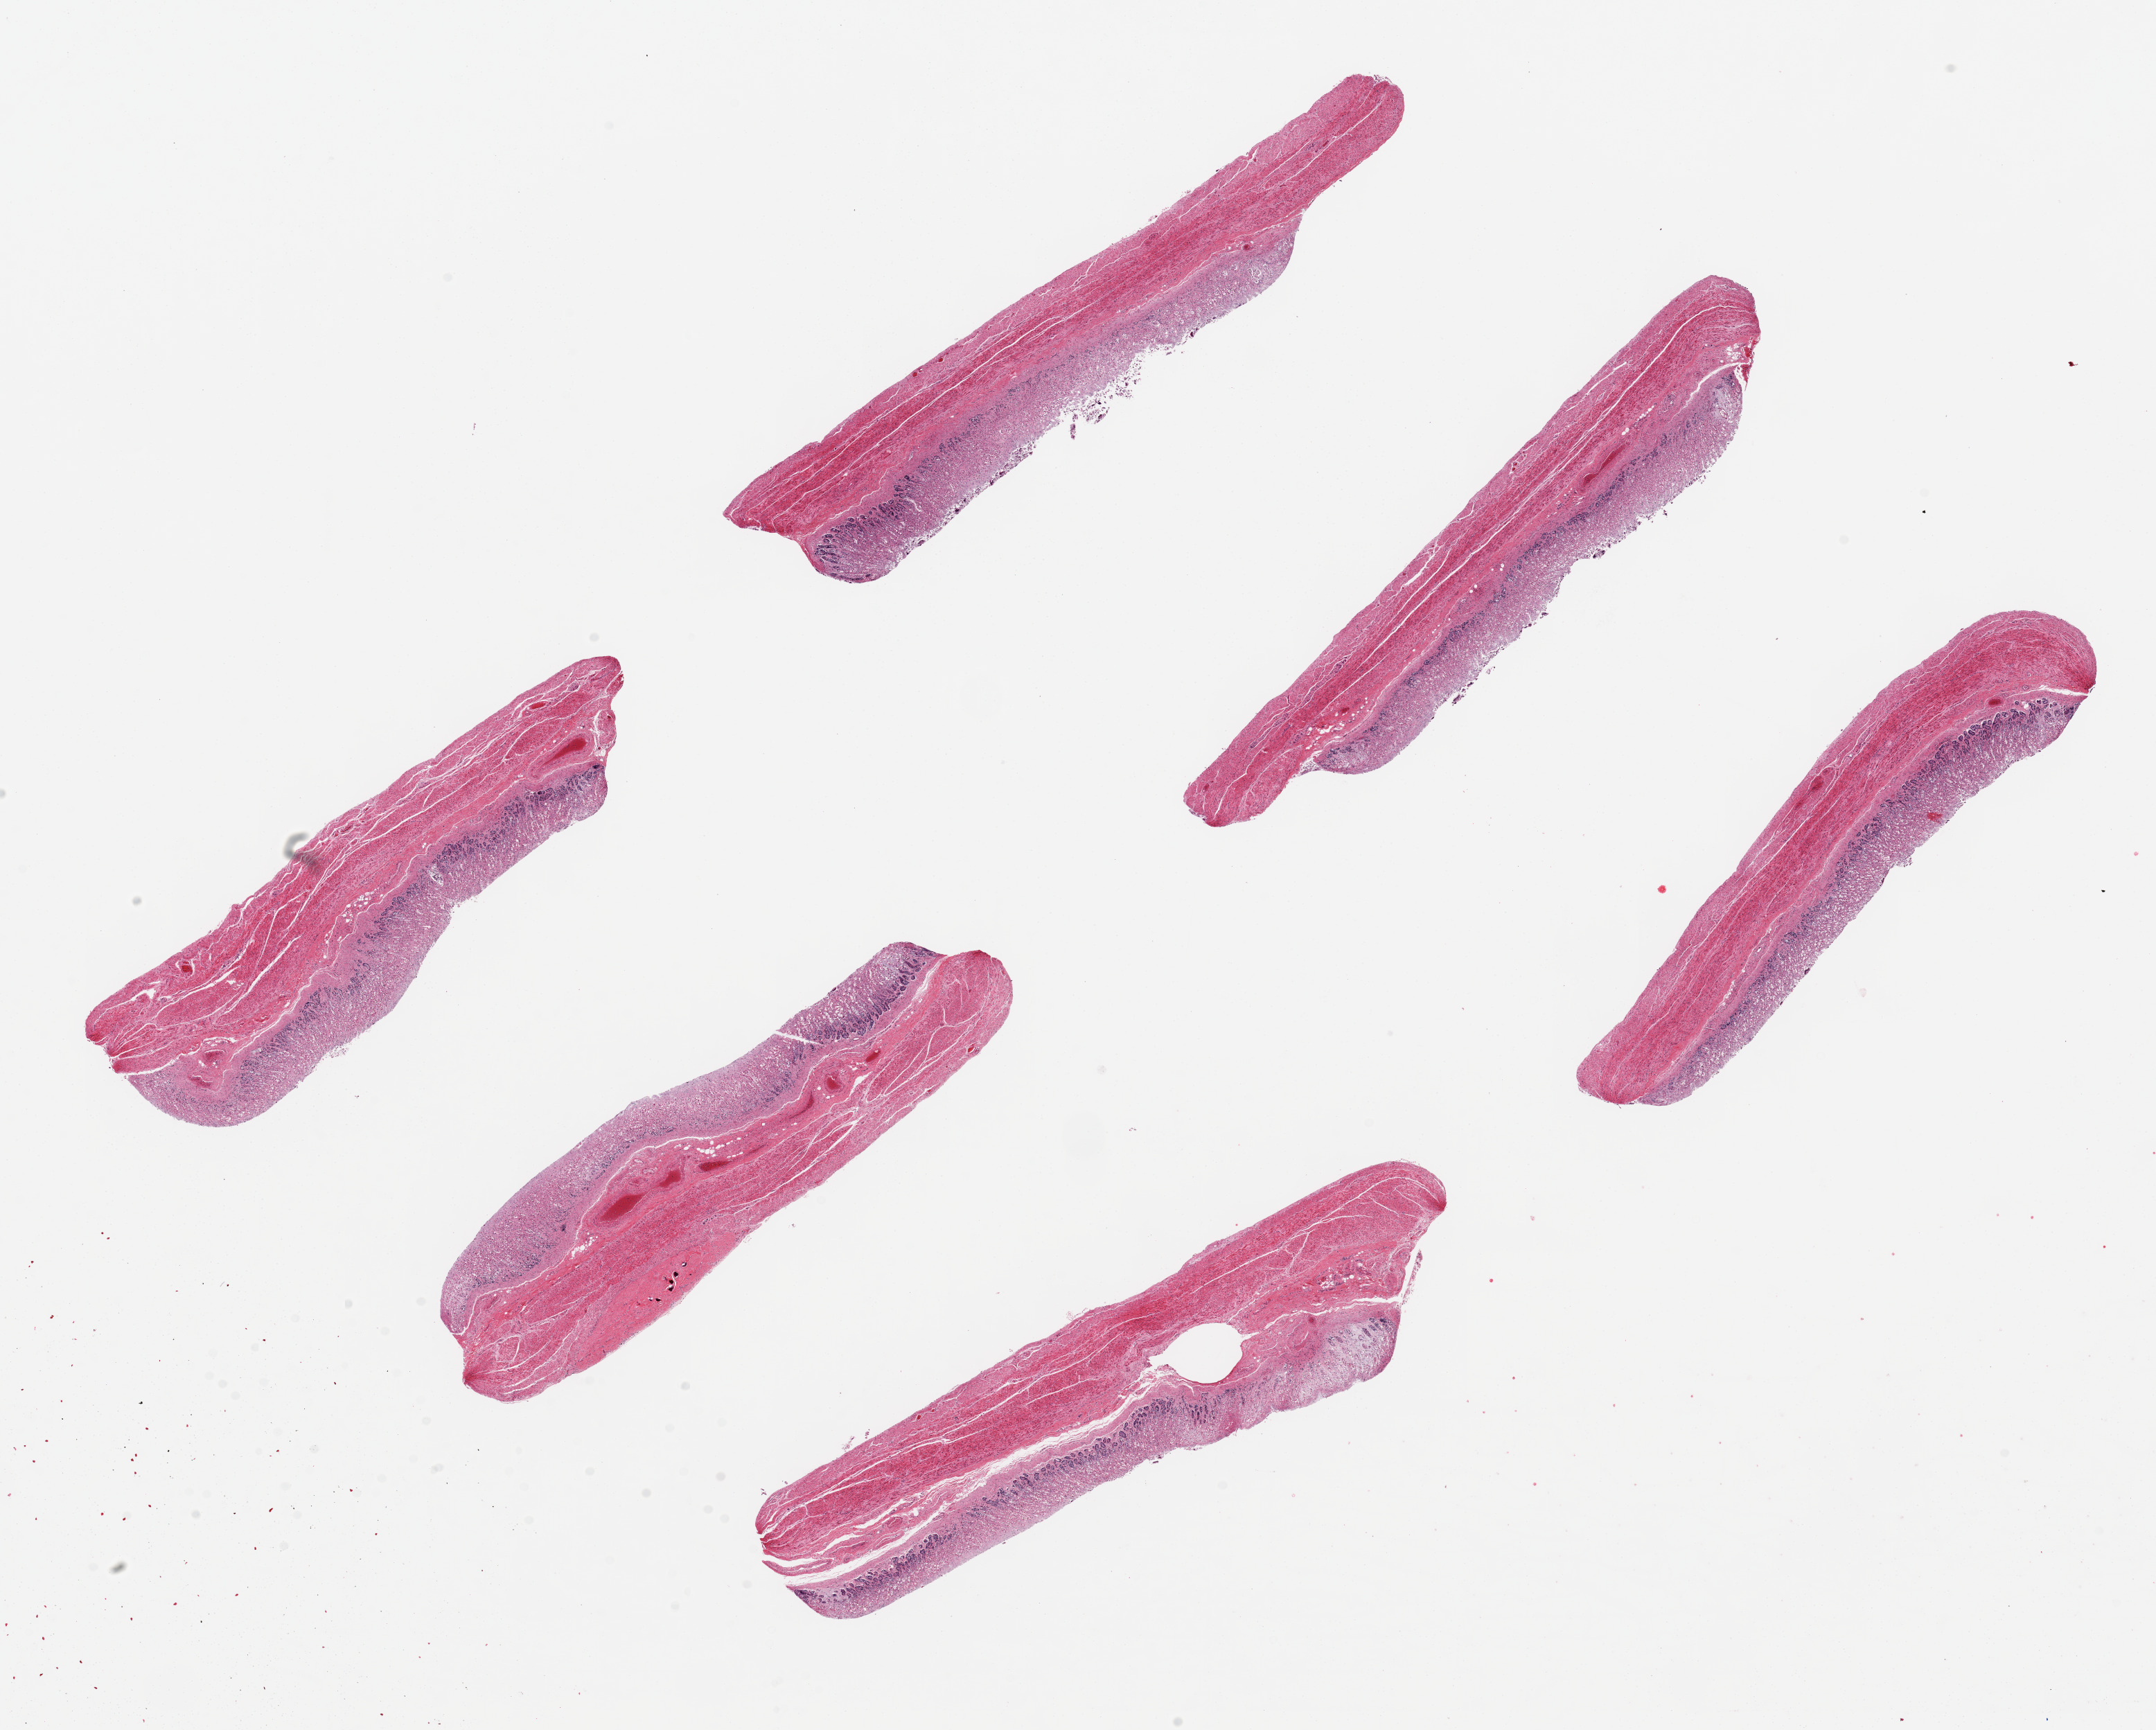
Haematoxylin and eosin whole-slide image — low-resolution overview of the scanned area, about 24.6 x 19.7 mm. PAXgene-fixed, paraffin-embedded tissue. Sampled site (target tissue): stomach. Donor tissue sample. Donor sex: female.
- review note (as recorded): 3(epithelium); 1-2 (muscularis); 6 ~ 7x2mm pieces; mucosa near totally autolysis, ~25-30% of thickness